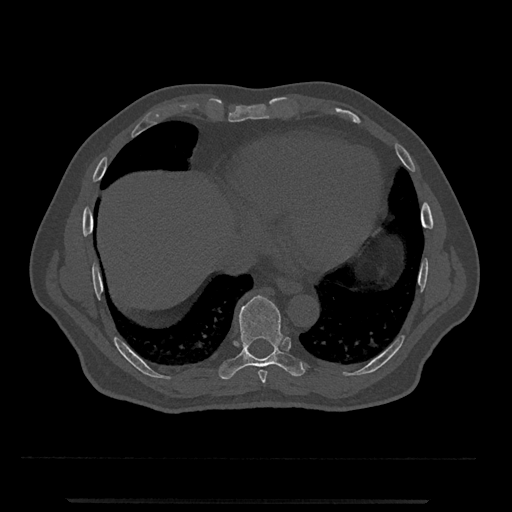
CT including the spine, one axial slice; slice 583 of 797 in the series (ordered by position); bone window (W 1800 / L 400 HU); 0.5 mm slice thickness; 512 × 512 image matrix, field of view 419 × 419 mm. Male patient, age 63 years. From the clinical record (not read from this slice): primary cancer: prostate.
Outlined on this slice (semi-automatically segmented with operator editing):
- T8 vertebra: bounding box (x1, y1, x2, y2) in pixels: (258, 370, 267, 383)
- T9 vertebra: (219, 295, 306, 380)